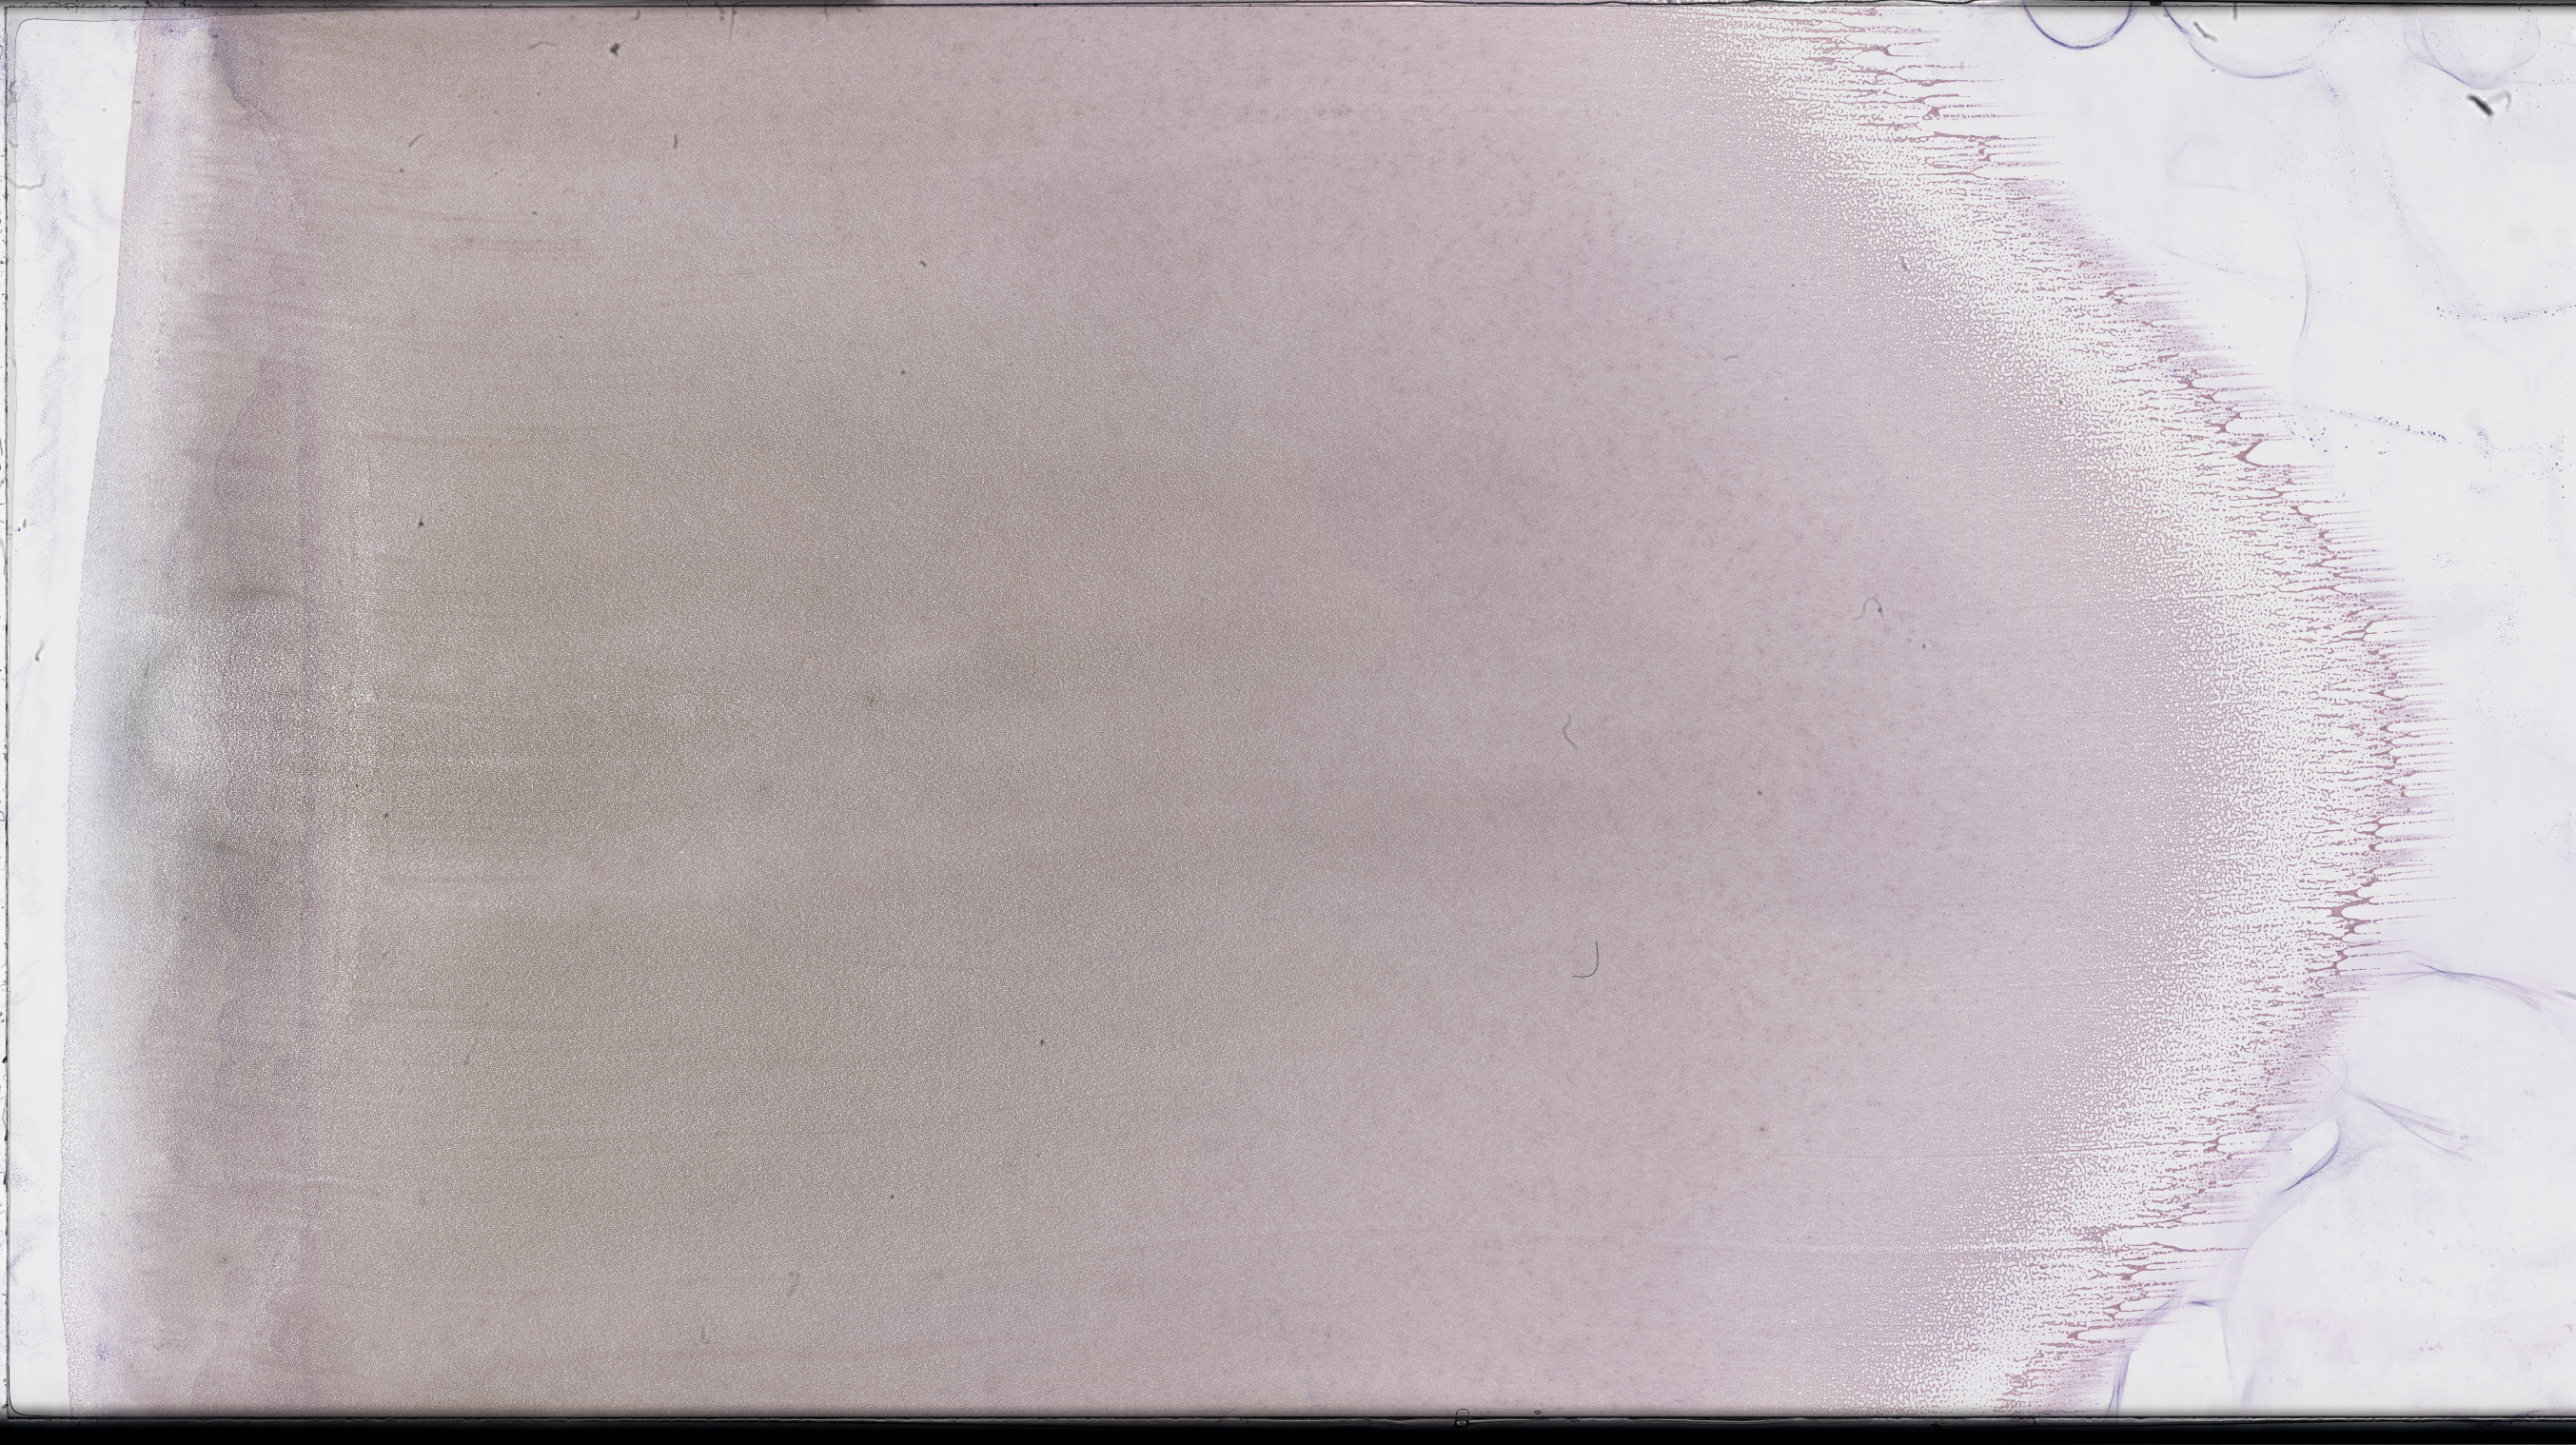
Whole-slide image of a whole blood smear, Wright–Giemsa stain, whole scanned area (about 43.7 x 24.5 mm) shown as a low-resolution overview. Smear from an EDTA sample. Collected on treatment. Patient sex: male.
Patient diagnosis: Plasma Cell Myeloma.